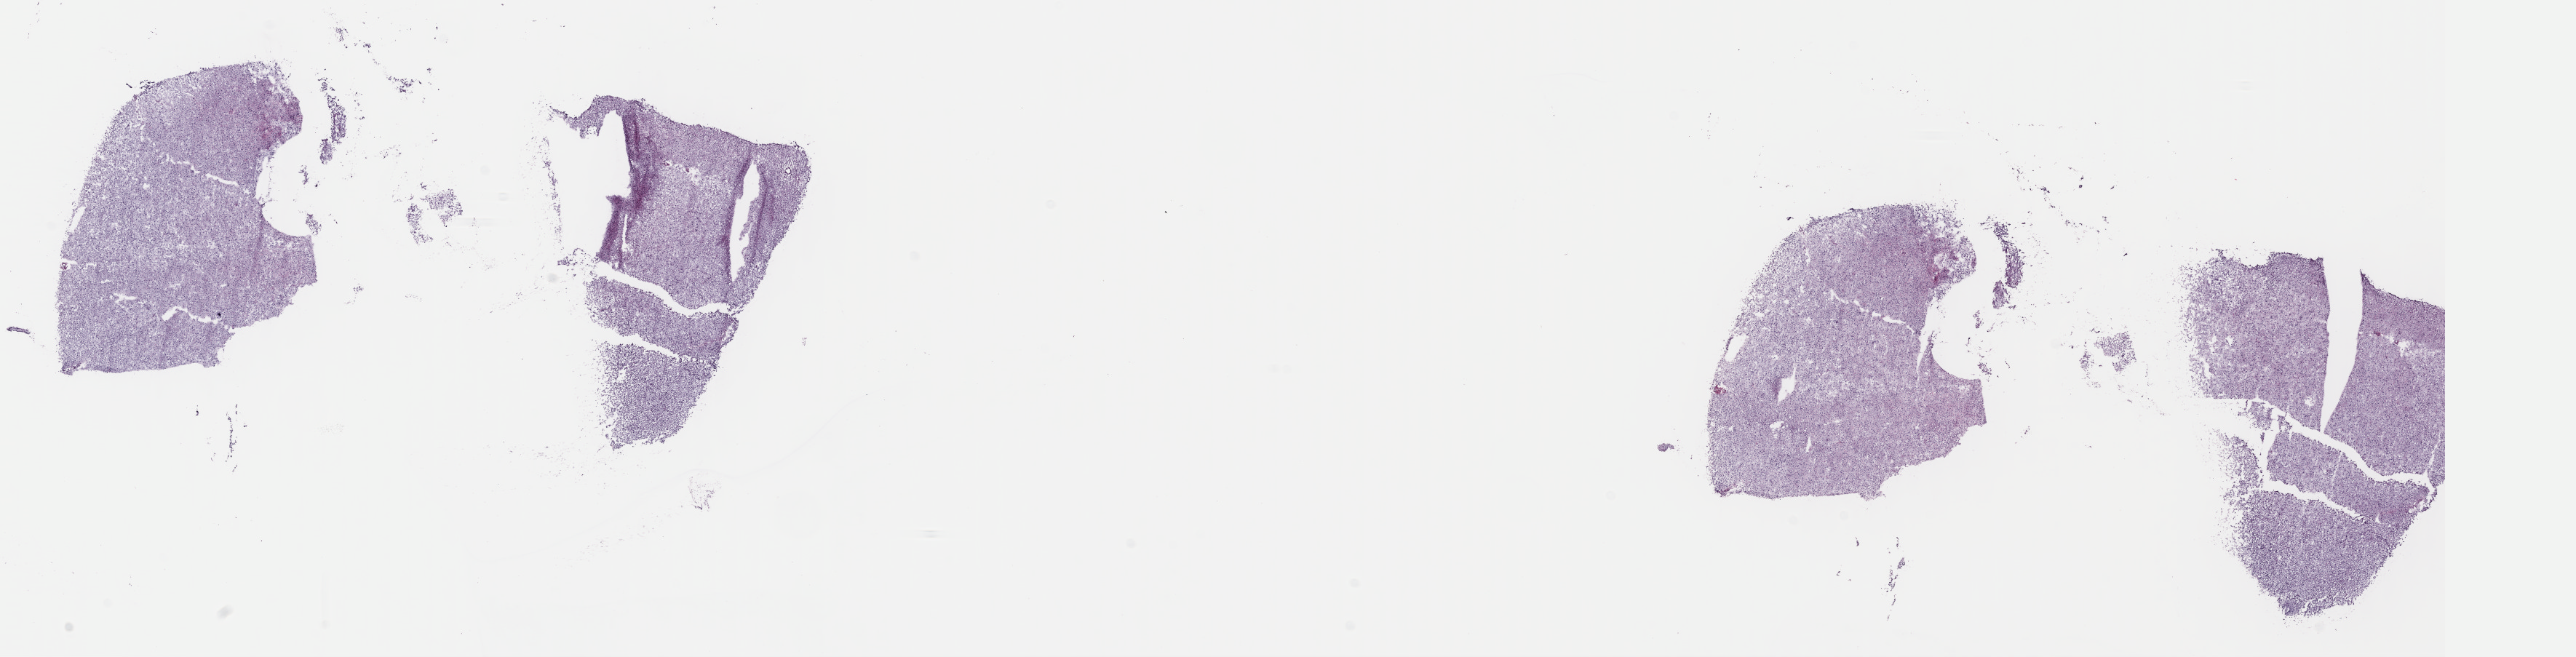
Whole-slide histology image, H&E-stained — a low-resolution overview of the entire scanned area, about 27.8 x 7.1 mm (slide scanned at 40x), frozen section from the top of the tissue portion, brain, primary tumour sample. Patient: female, age at initial diagnosis 24 years. Histologic grade: G2 (moderately differentiated). Slide review estimates, as recorded: tumour cells 80%, tumour nuclei 85%, normal cells 10%, stromal cells 10%, necrosis 0%. Inflammatory infiltration, as recorded: lymphocyte infiltration 0%, monocyte infiltration 0%, neutrophil infiltration 0%.
* histologic diagnosis: Oligodendroglioma, NOS (cerebrum)